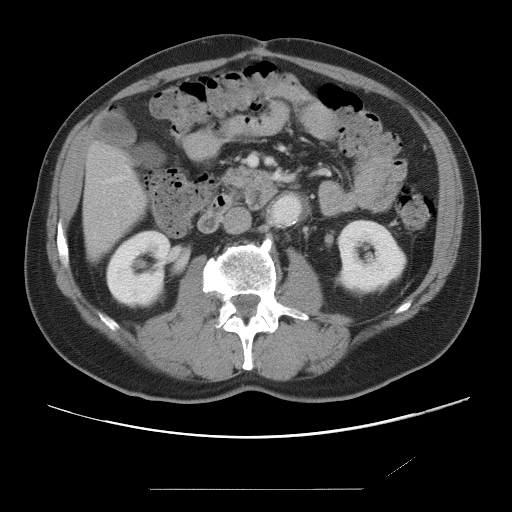
Contrast-enhanced abdominal CT, one axial slice; position 18 of 87 along the scan axis; 120 kVp; intravenous contrast given; soft-tissue window (W 400 / L 40 HU); 512 × 512 image matrix, field of view 406 × 406 mm. Male patient, age 74 years. From the clinical record (not read from this slice): diagnosis: colorectal cancer liver metastases, imaged before liver resection; multiple liver metastases: yes; largest metastasis: 1.1 cm.
Outlined on this slice (manually delineated by an expert):
- hepatic veins: bounding box (x1, y1, x2, y2) in pixels: (113, 178, 119, 181)
- liver: (84, 146, 144, 256)
- planned liver remnant (the part of the liver to remain after resection): (84, 146, 144, 255)